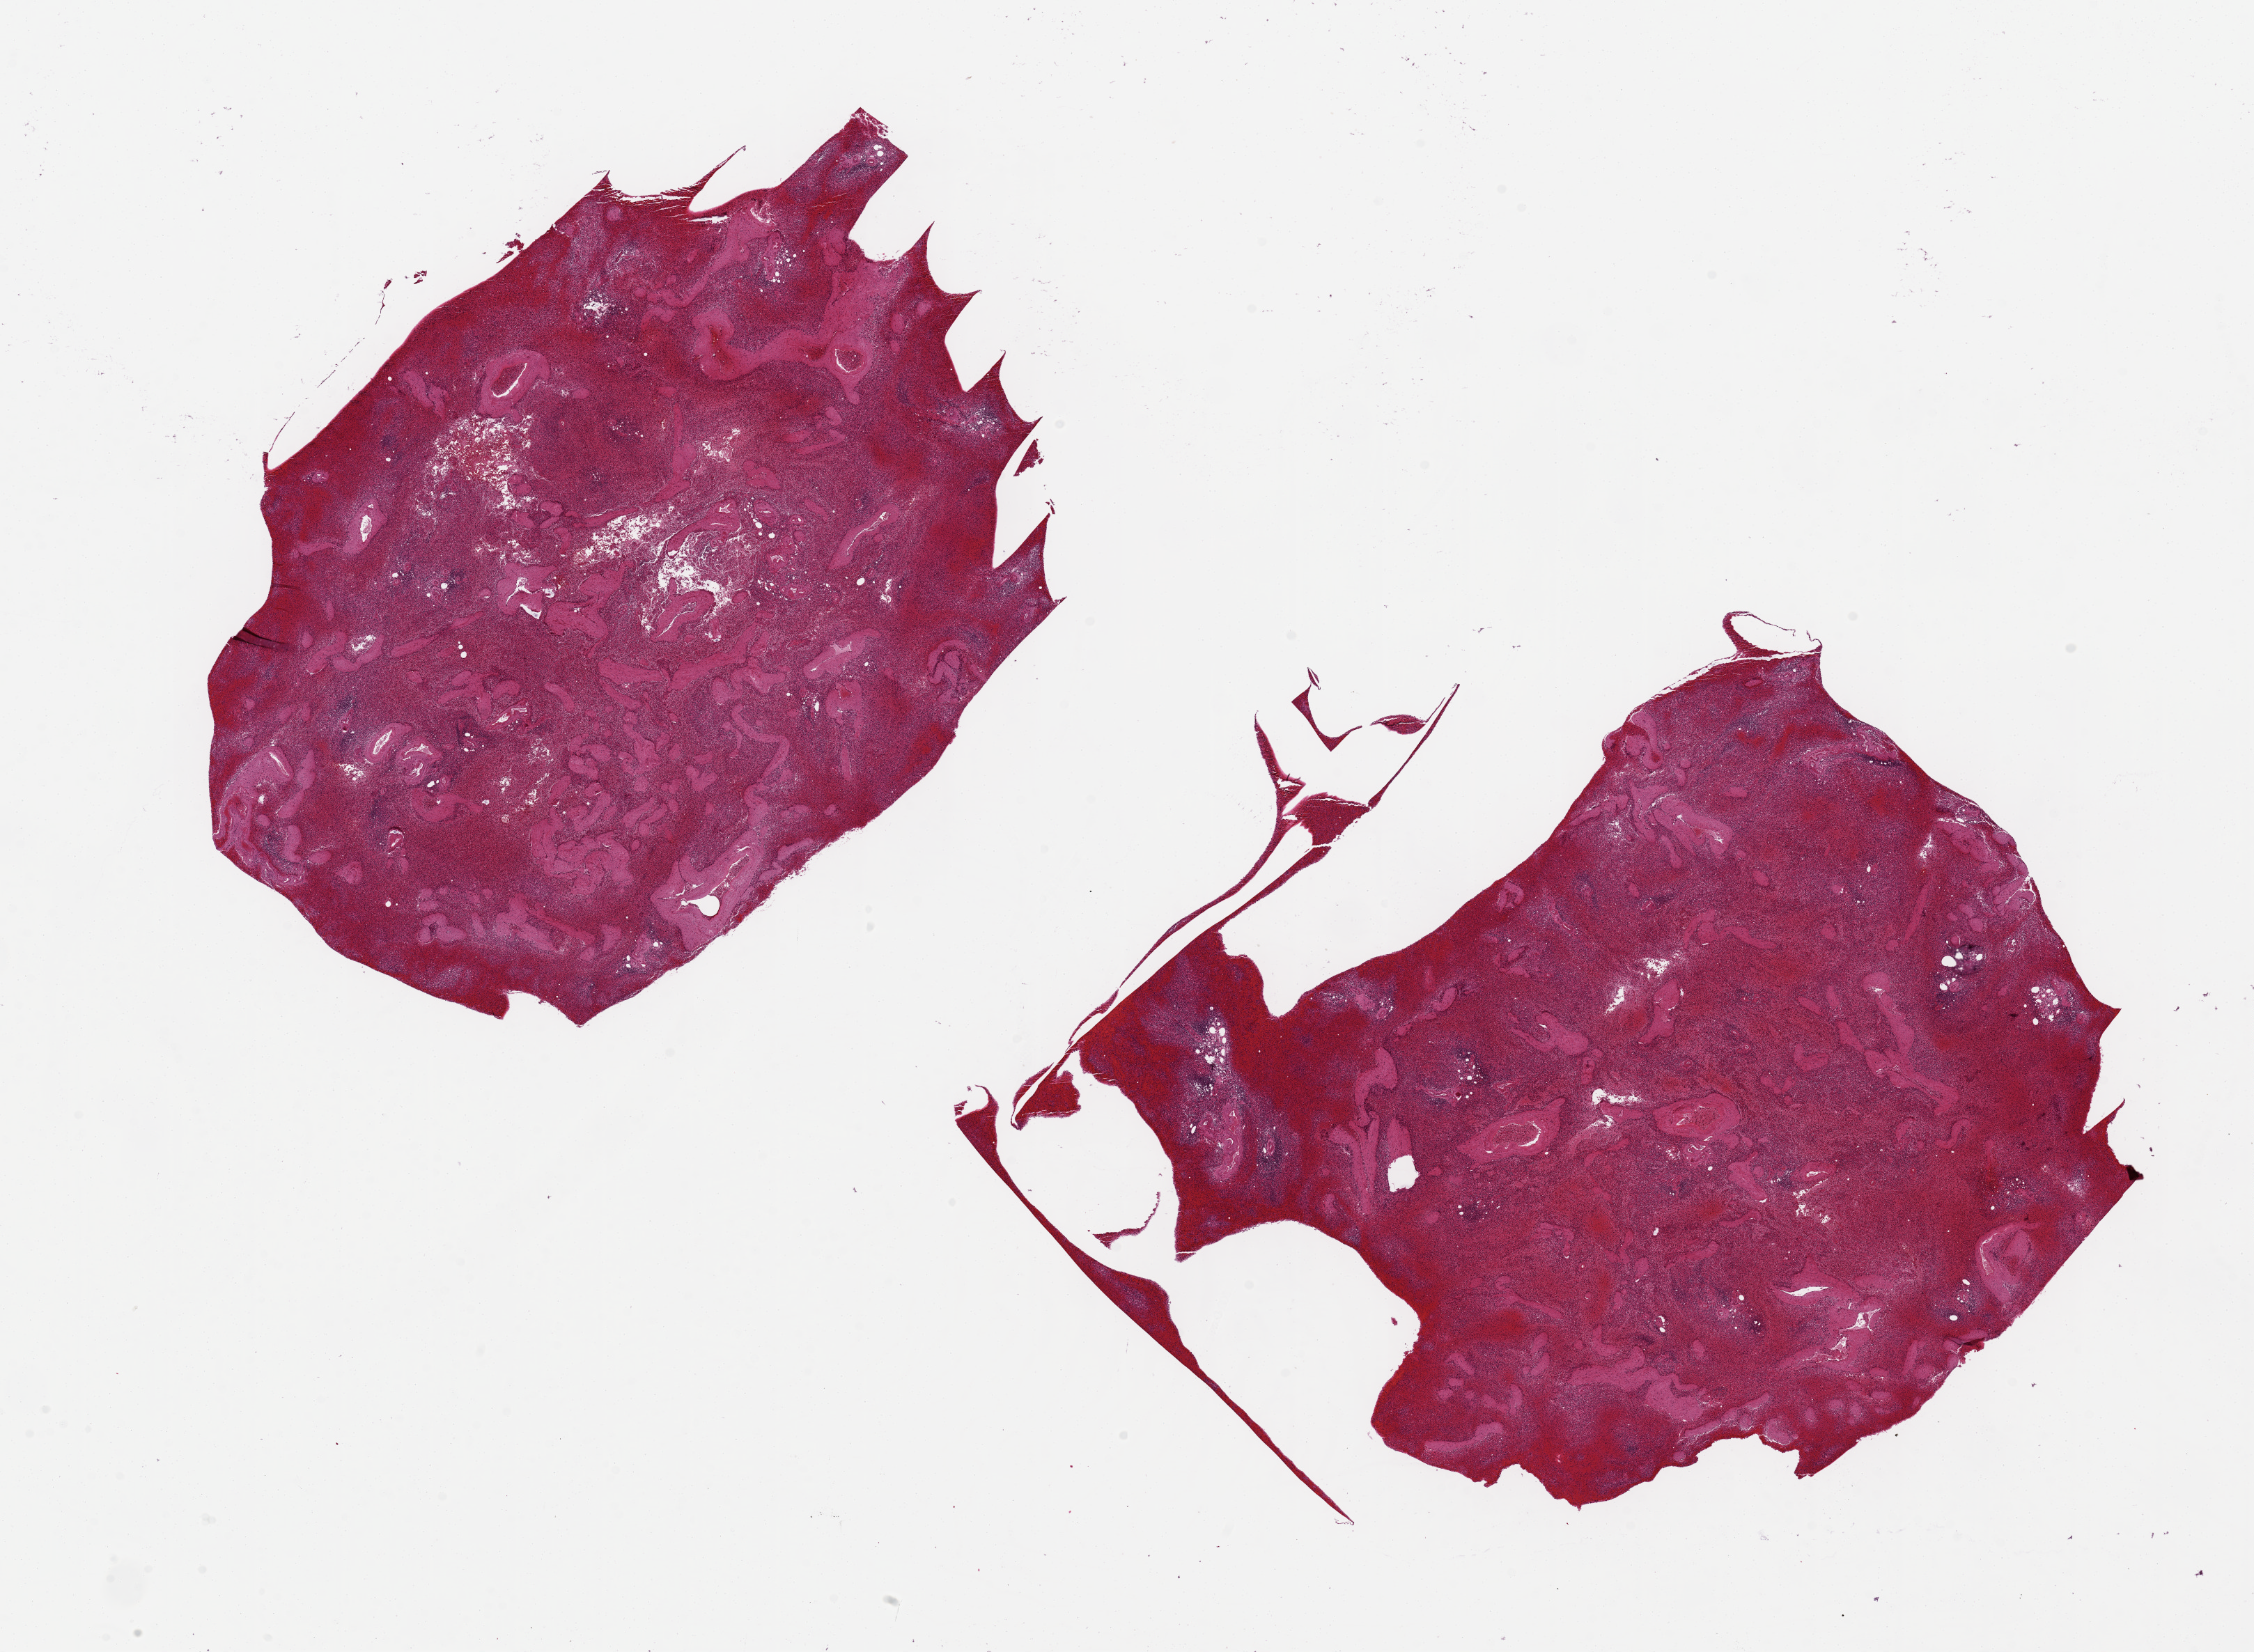
Haematoxylin and eosin whole-slide image, brightfield, shown as a low-resolution overview of the whole scanned area (about 25.6 x 18.8 mm, from a 20x scan). PAXgene-fixed, paraffin-embedded tissue. Sampled site (target tissue): spleen. Tissue donor sample. Female donor.
- pathologist's review note for this sample: 2 aliquots, ~10x7. Severe congestion, badly autolyzed